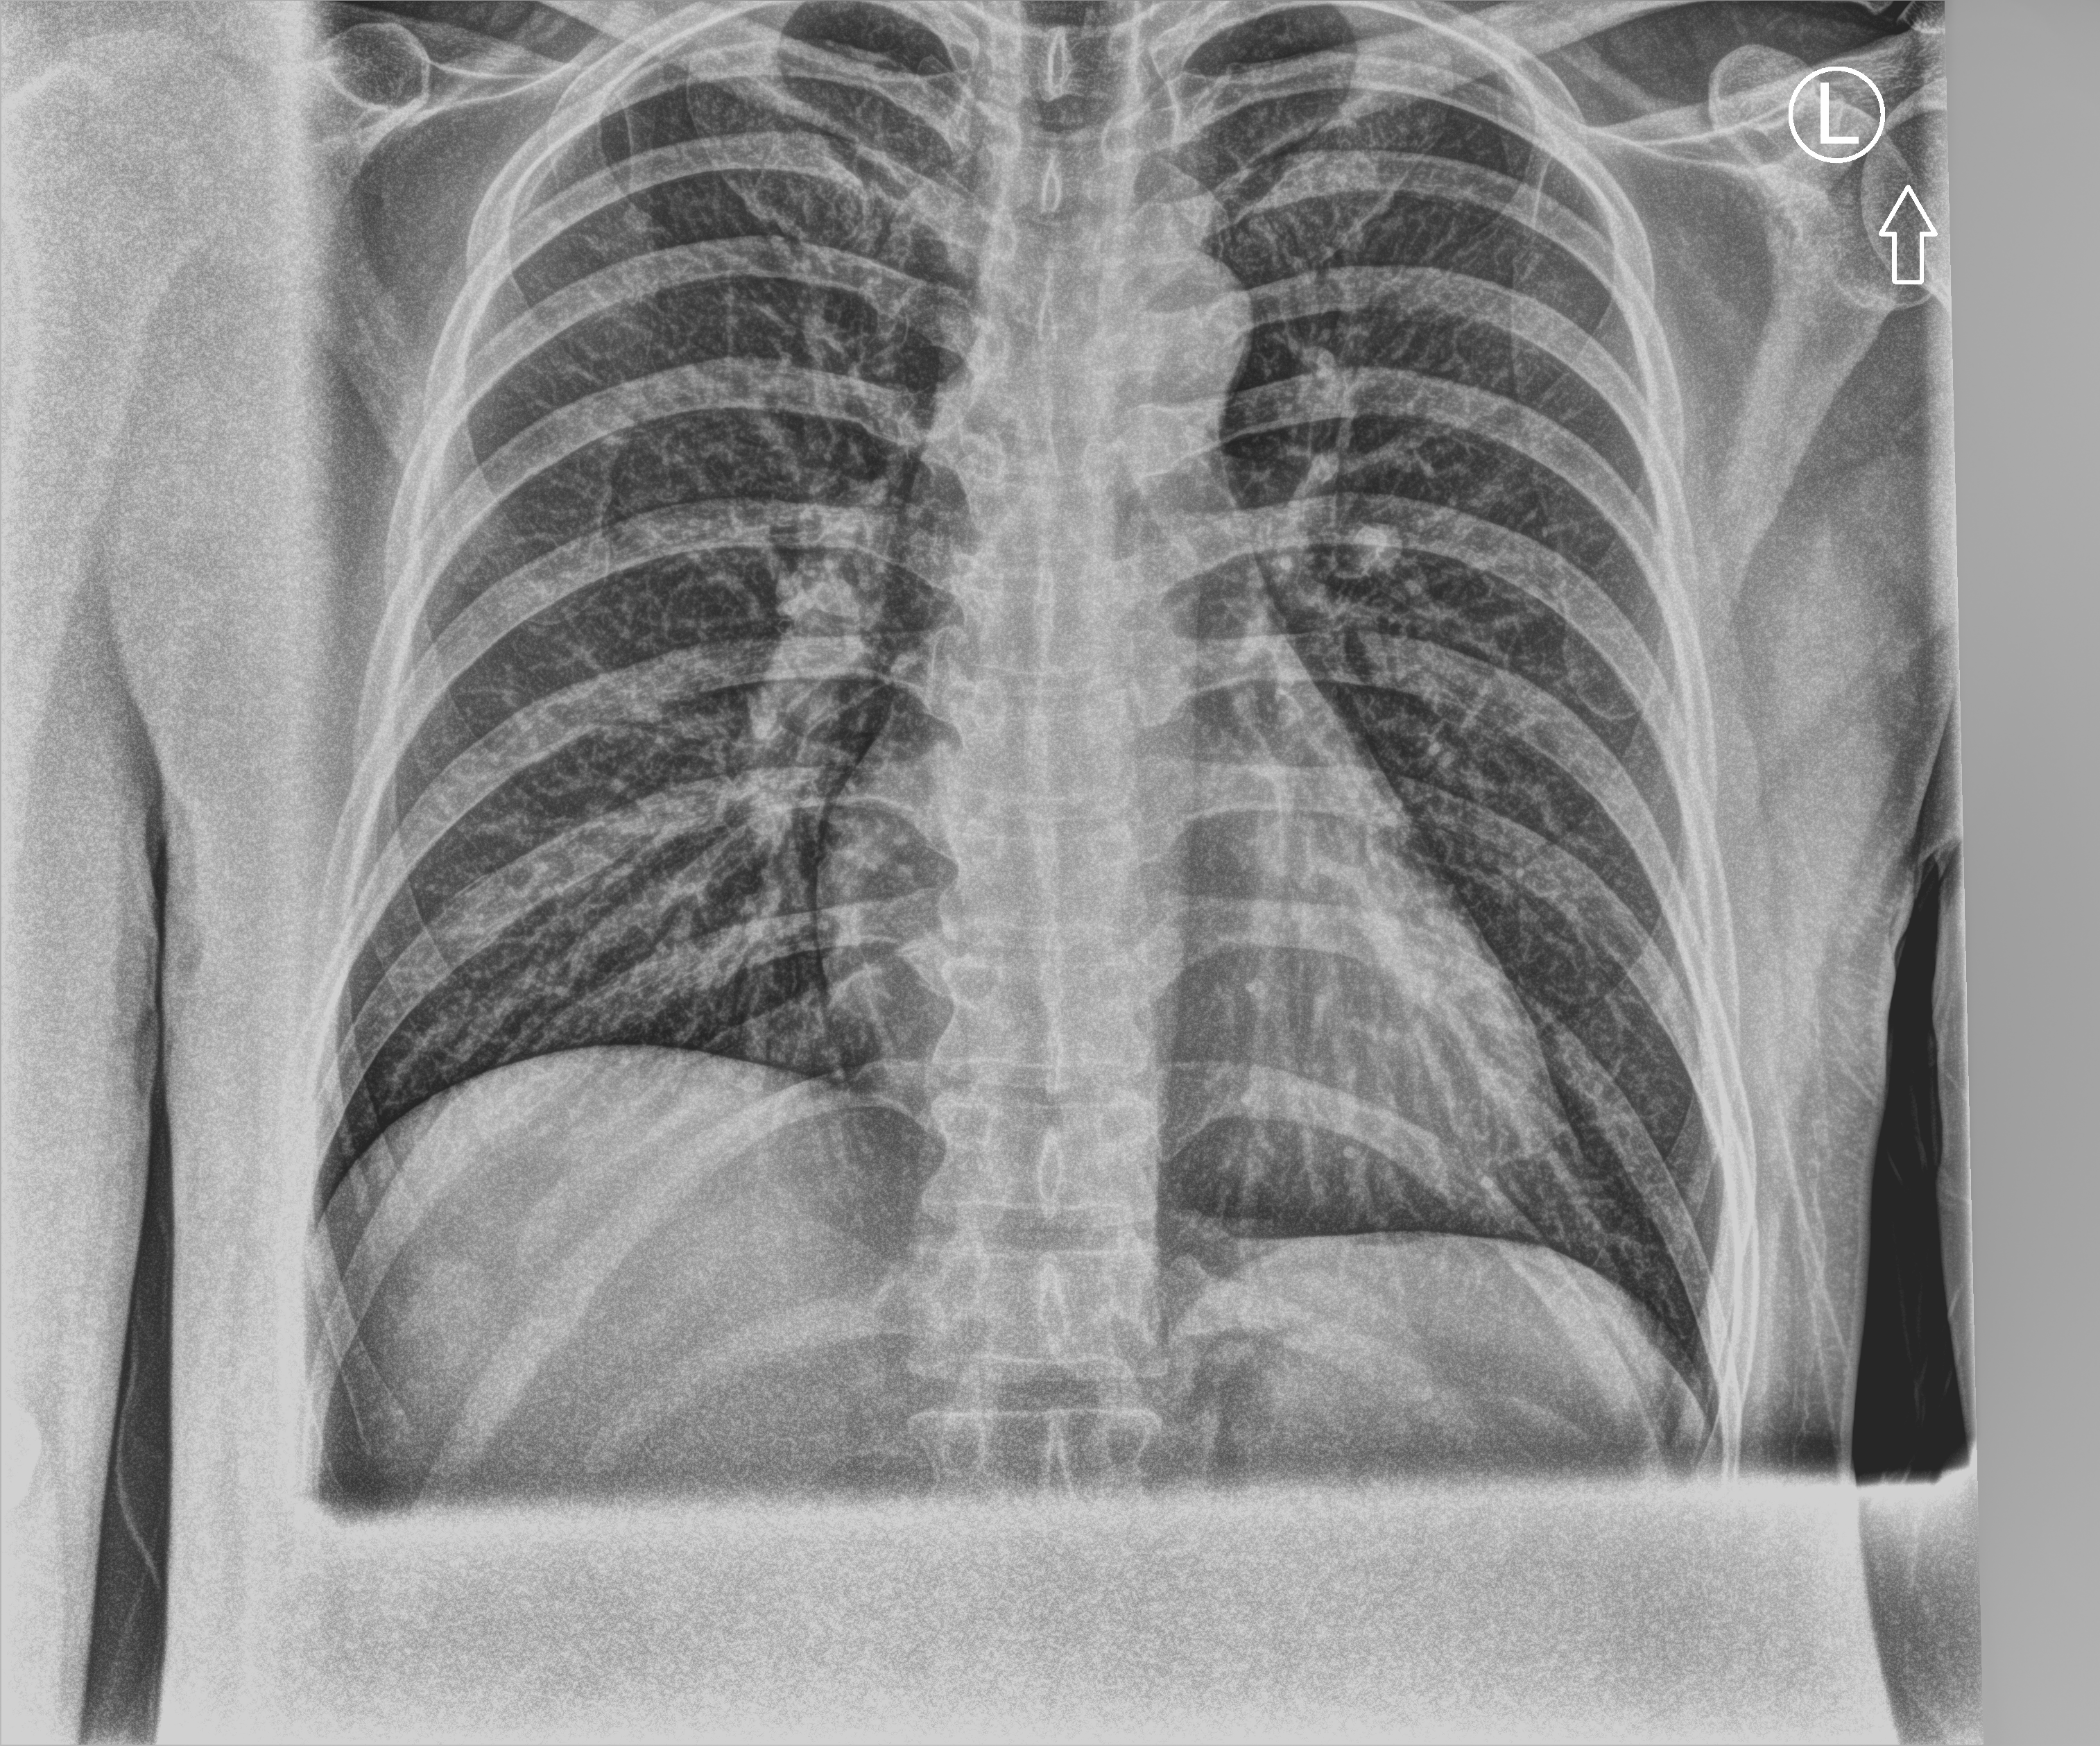
Chest X-ray (portable), anteroposterior (AP) projection. Patient hospitalised with COVID-19; male, aged 18–59 years.
Admission-level facts for this patient (not findings on this image; timing relative to this image not recorded): mechanically ventilated during this hospital stay: no.